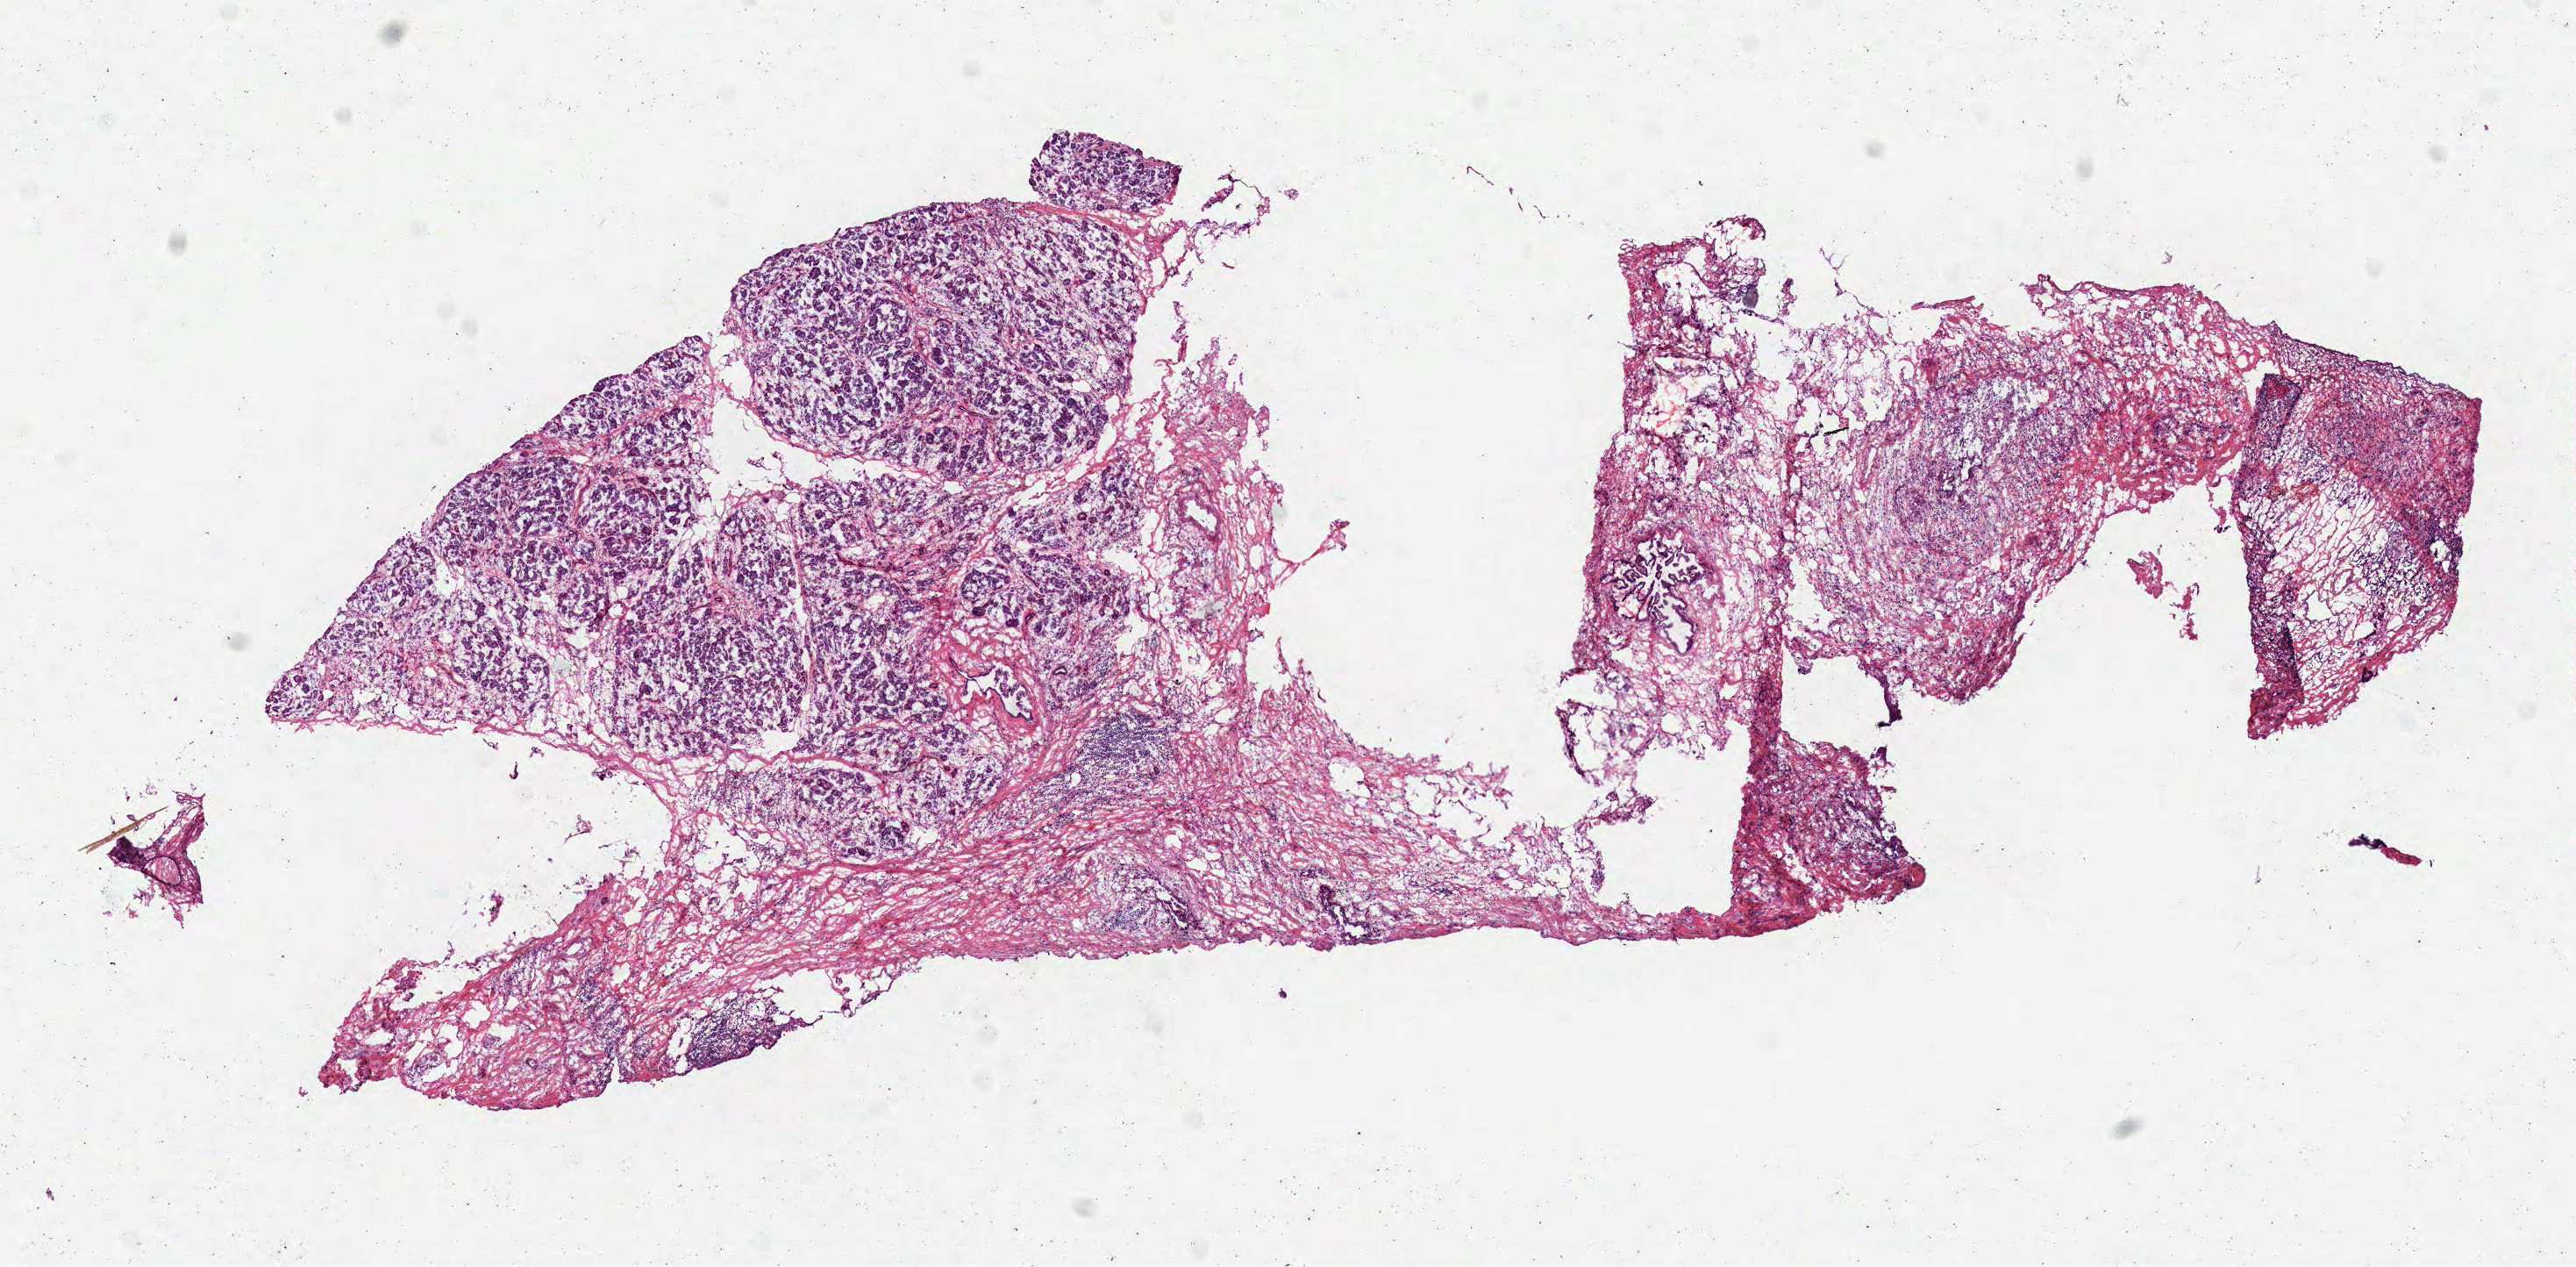
Whole-slide histology image, H&E, whole scanned area (about 11.8 x 5.8 mm) shown as a low-resolution overview. Frozen section. Pancreas, primary tumour sample. Female, age 79 years at initial diagnosis. Slide review estimates, as recorded: tumour cells 30%, tumour nuclei 15%.
Histologic diagnosis: Infiltrating duct carcinoma, NOS (head of pancreas).